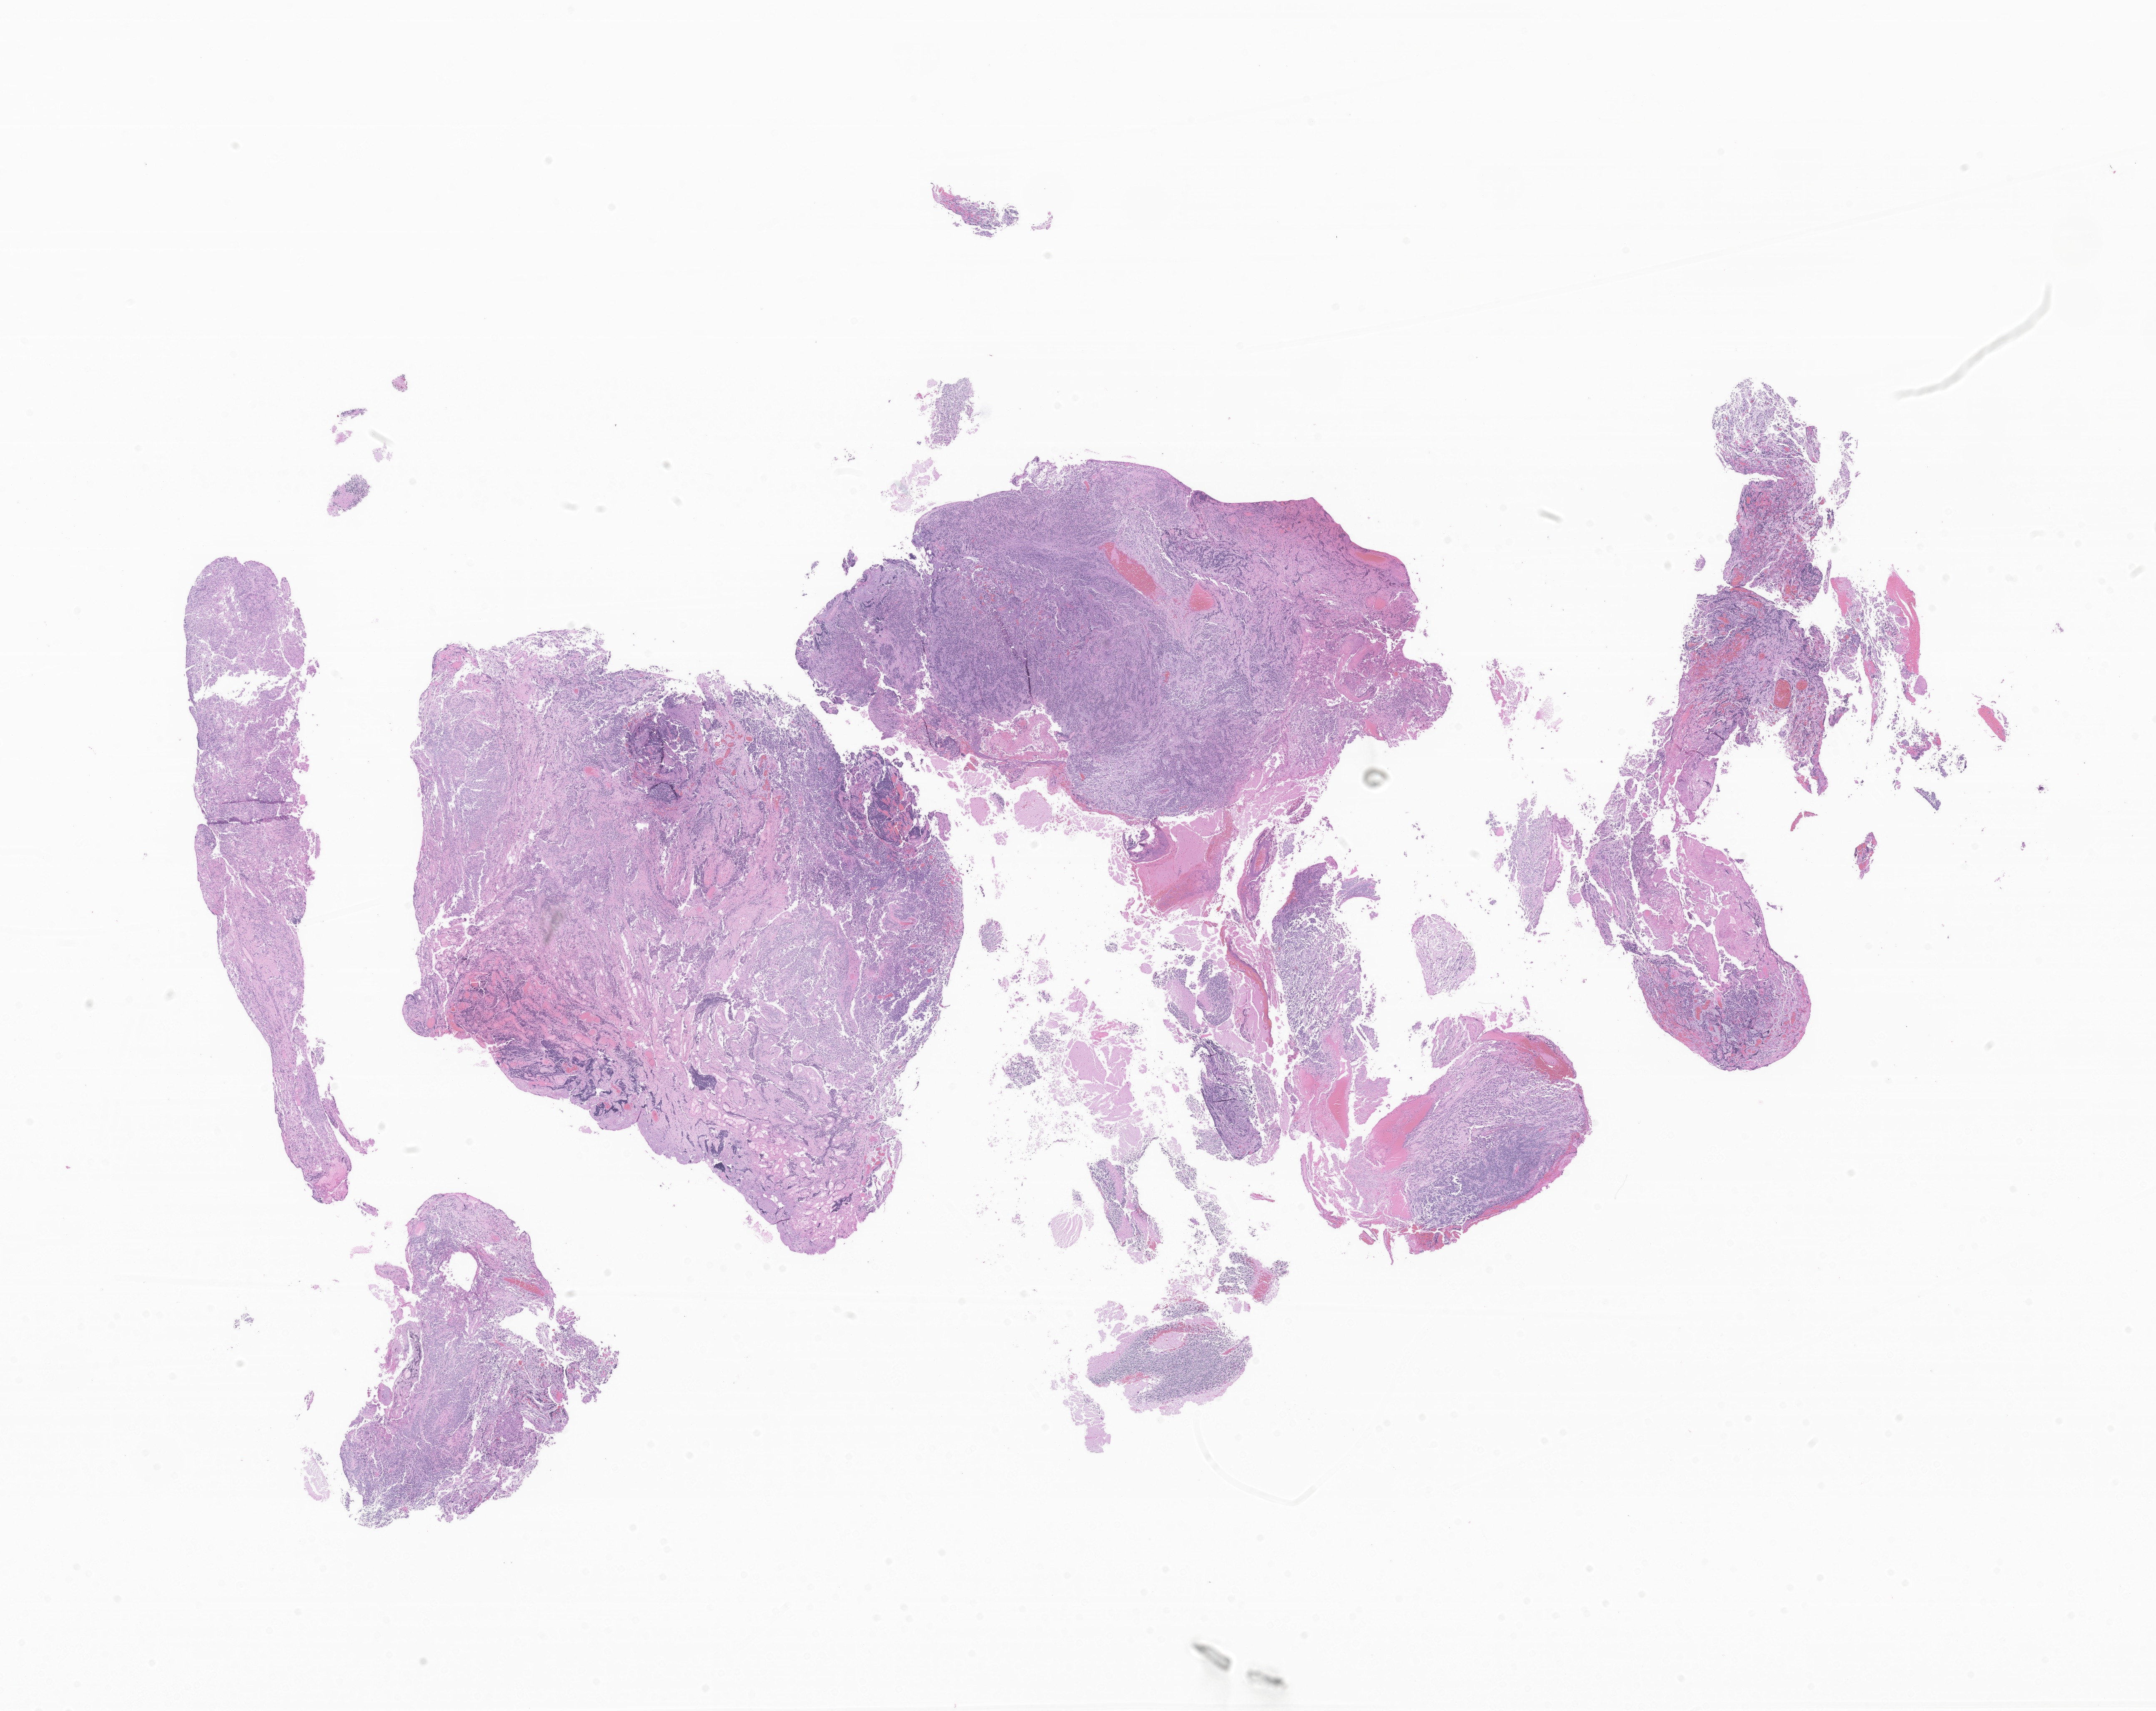
Digitized haematoxylin and eosin-stained section of tumor tissue from the brain — shown as a low-resolution overview of the whole scanned area (about 21.8 x 17.3 mm). Formalin-fixed, paraffin-embedded (FFPE) tissue. Male patient, age 578 days.
Diagnosis: Neoplasm, benign.